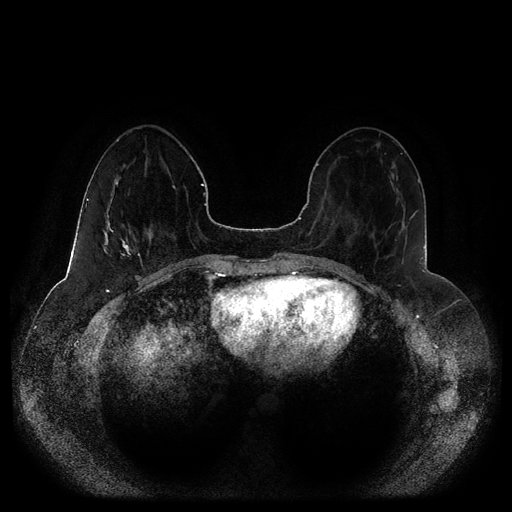
Breast MRI (dynamic contrast-enhanced, multi-phase), one axial slice. Position 36 of 116 along the scan axis. Dynamic contrast-enhanced series, time point 2 of 5 at this slice position (early post-contrast). 1.5 T. TE 2.5 ms, TR 5.2 ms. 2 mm slice thickness. 512 × 512 image matrix, field of view 390 × 390 mm. Female patient, age 44 years.
Outlined on this slice (semi-automatically segmented with operator editing):
- breast lesion (labelled 'tumour' in the annotation; benign lesions carry a separate 'benign' label): box from (x=102, y=182) to (x=133, y=266) px